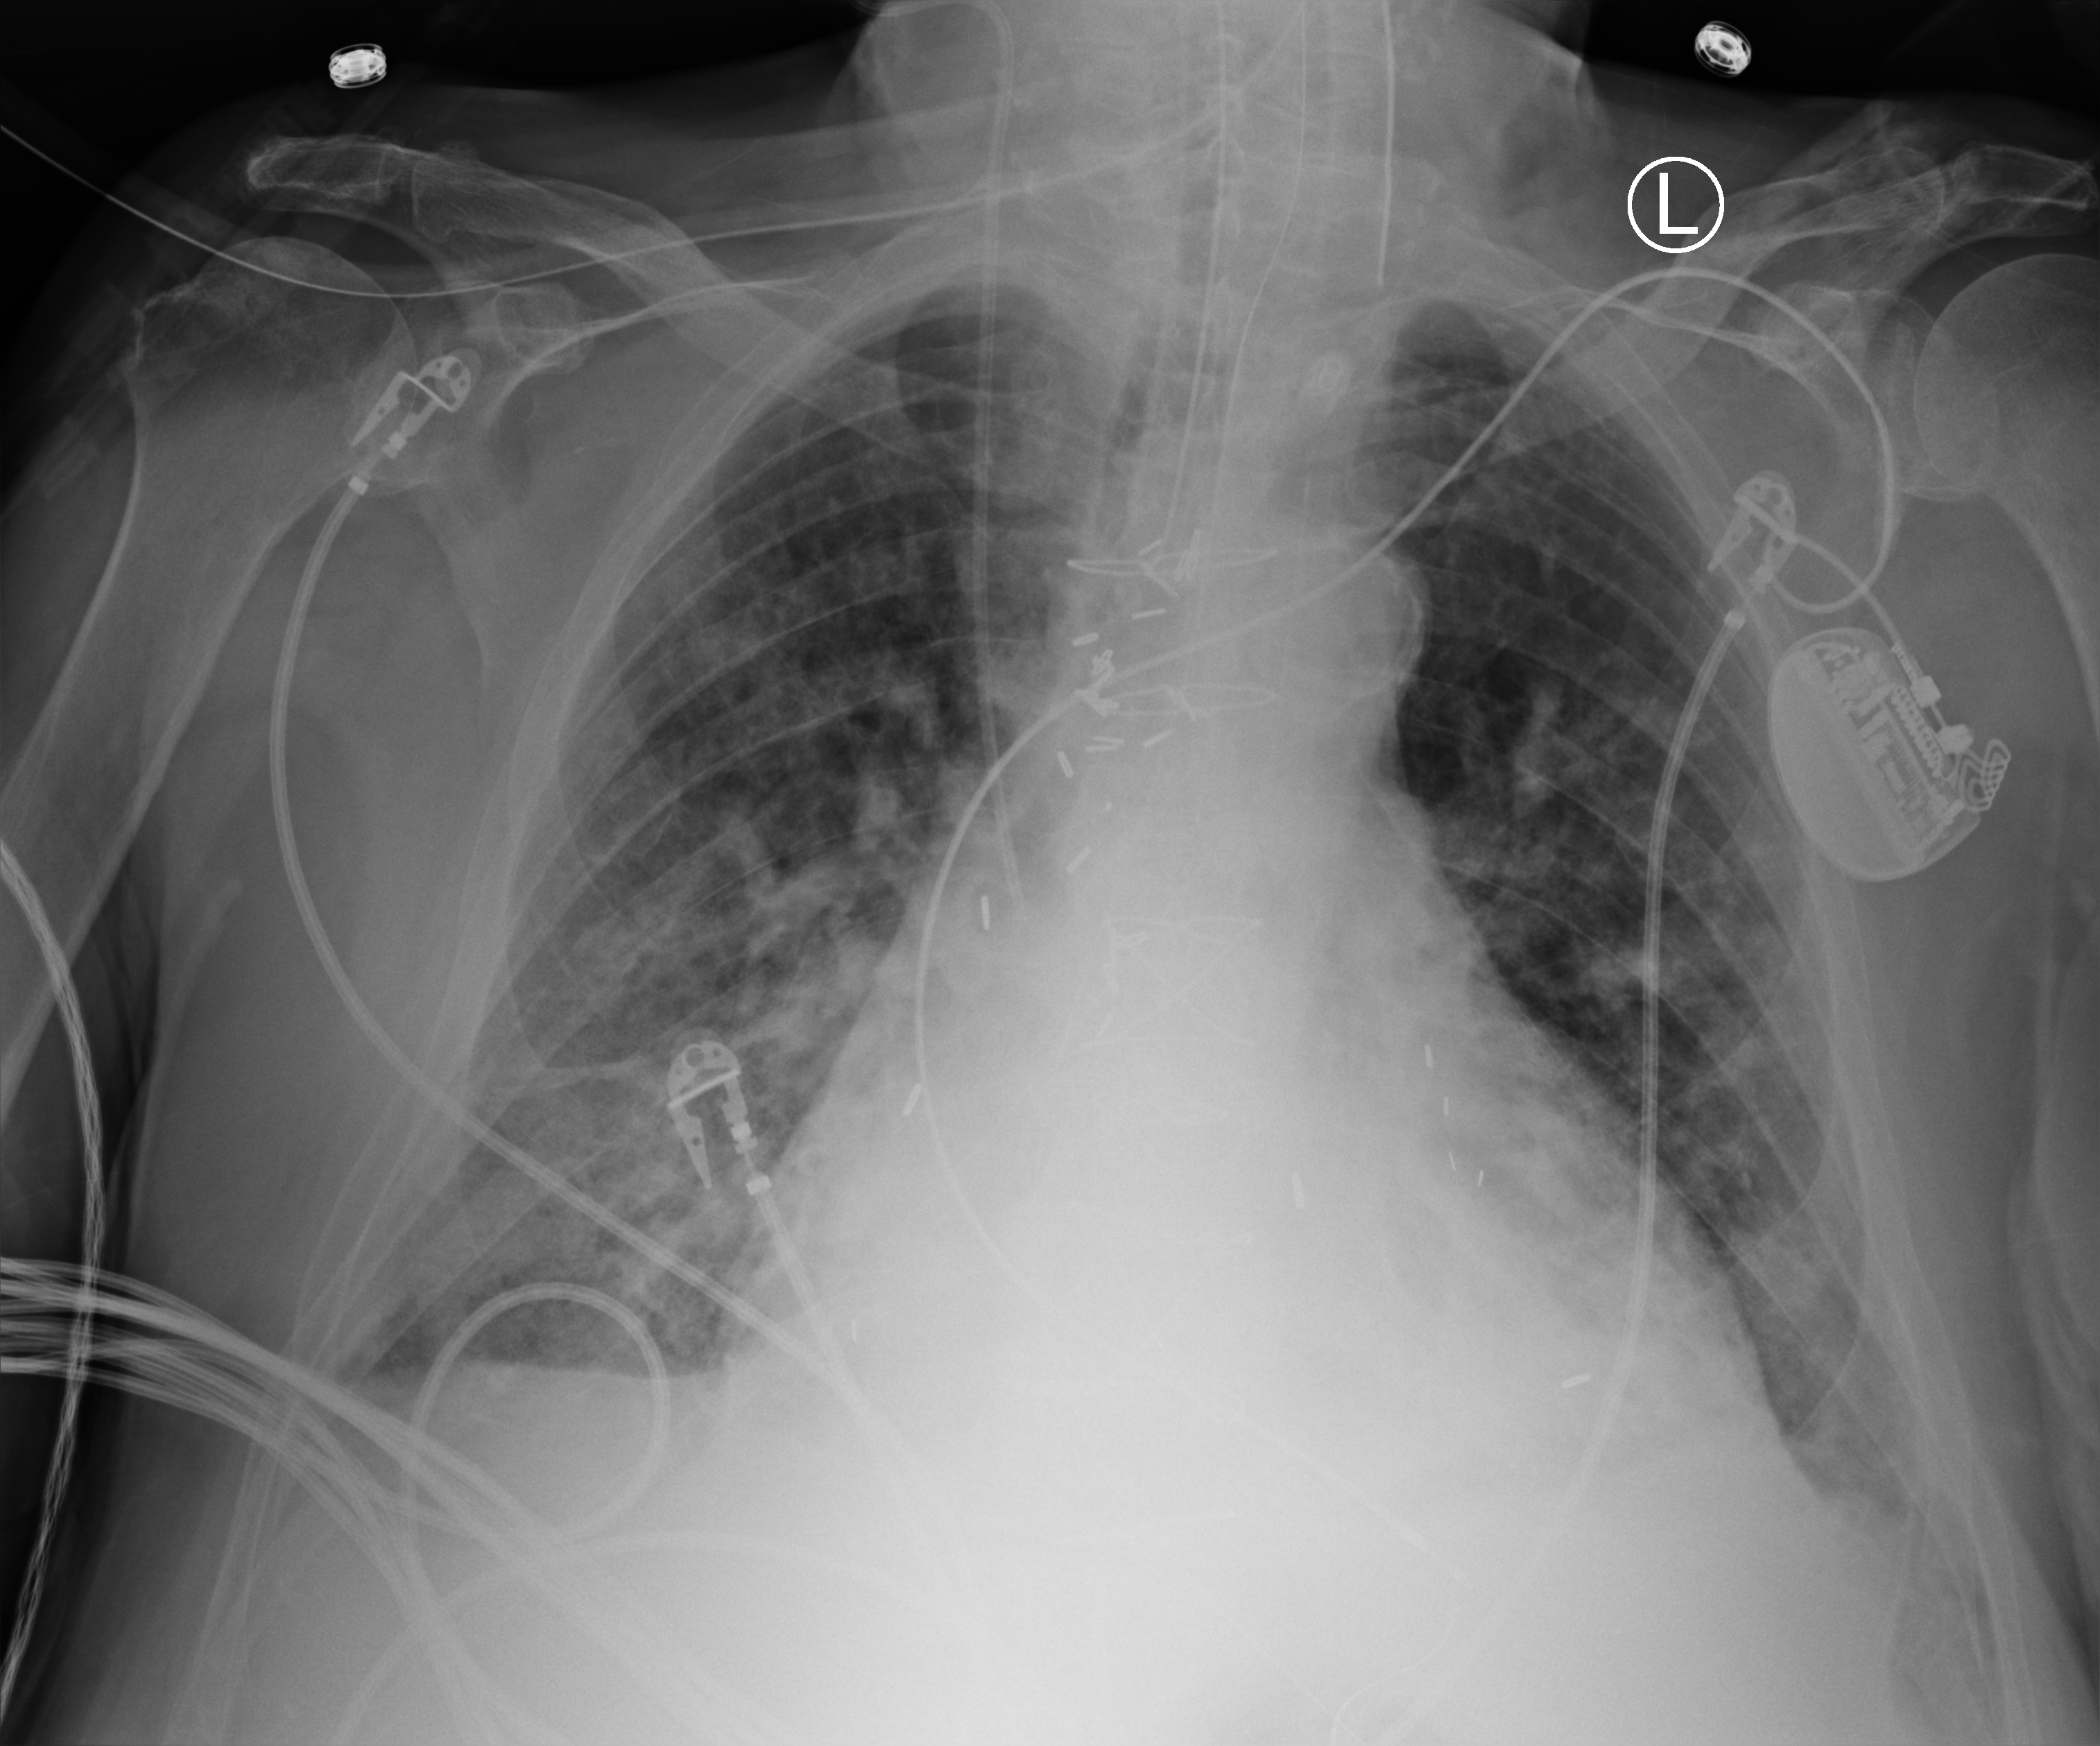
Bedside chest radiograph (computed radiography), anteroposterior (AP) projection. Patient hospitalised with COVID-19; male, aged 75–90 years.
Hospital-stay facts (about this admission, not read from this image; timing relative to this image not recorded):
- smoking status (admission record): former
- admitted to intensive care during this hospital stay: yes